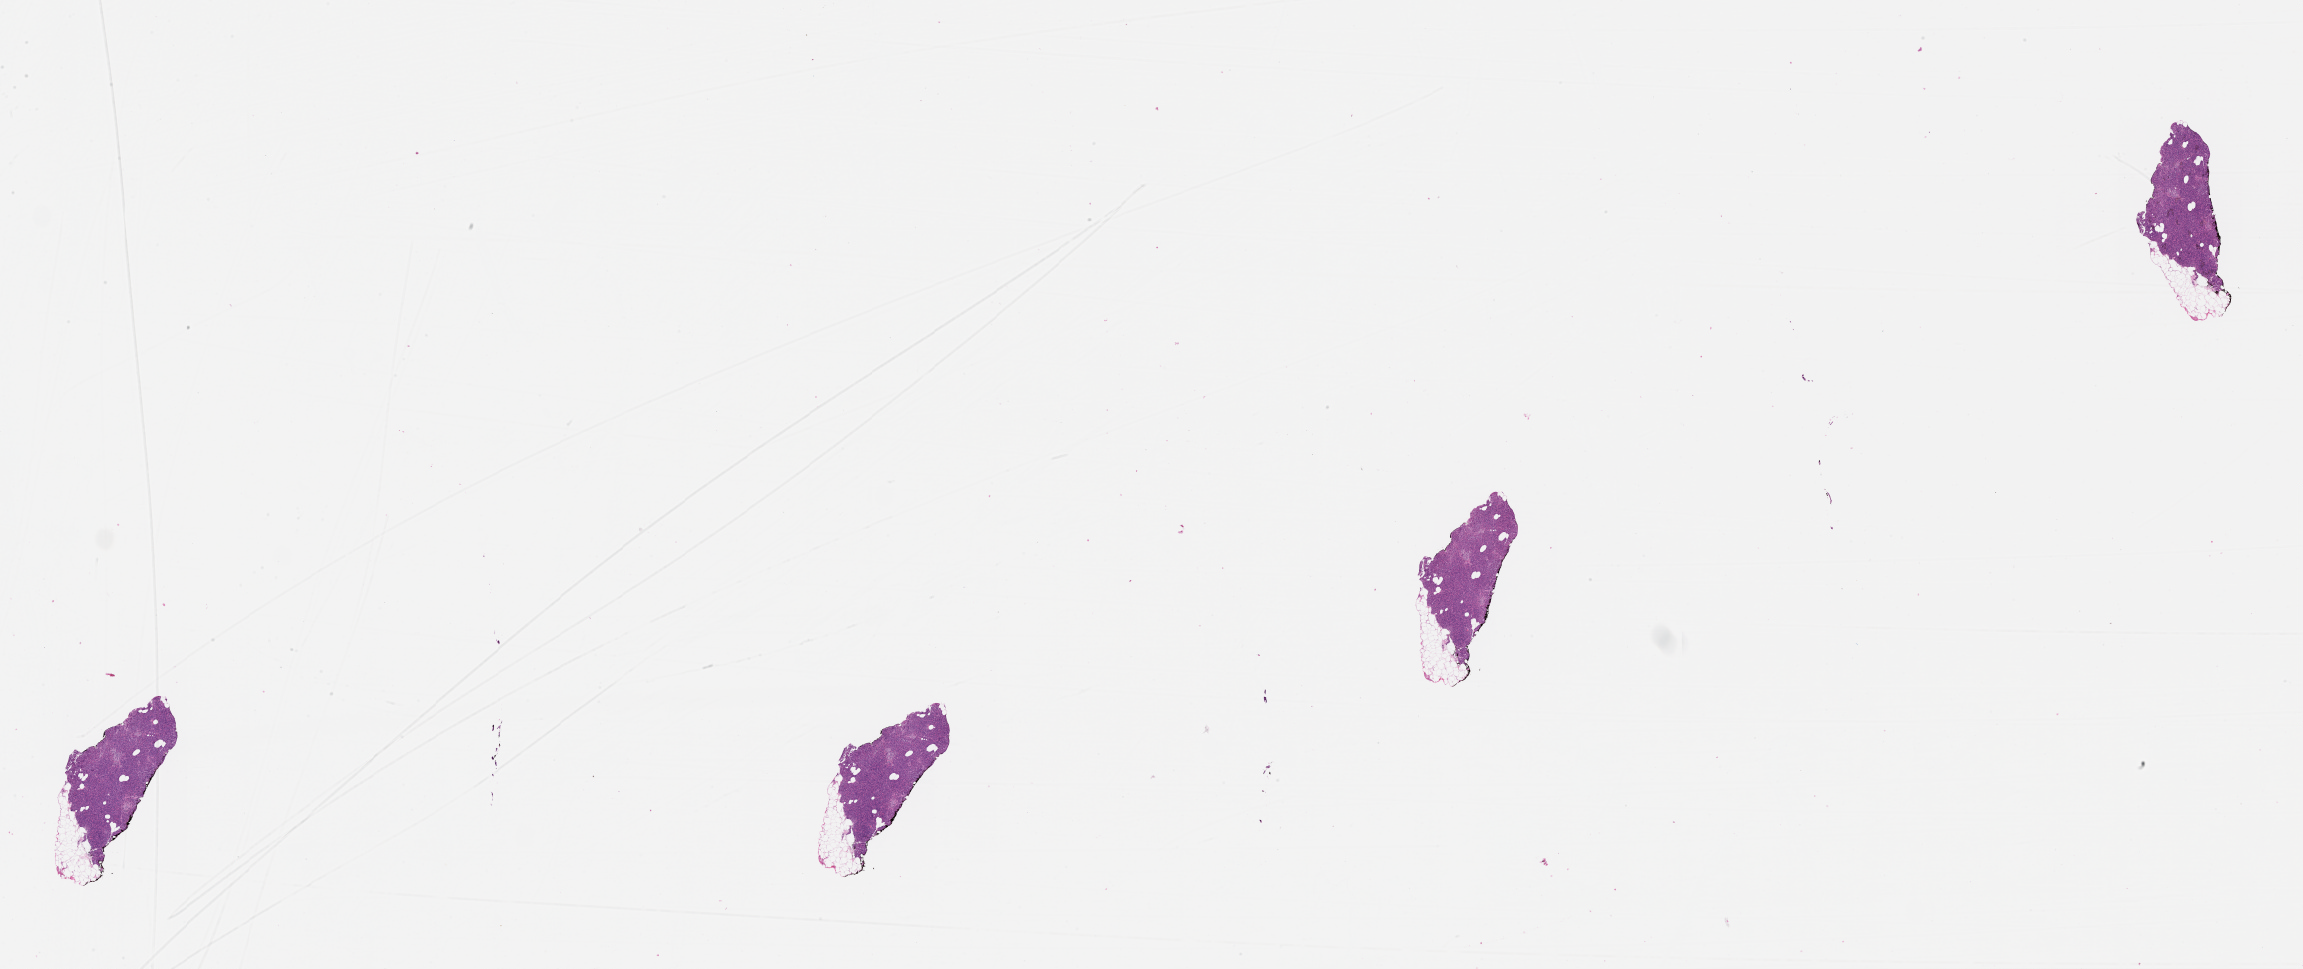
Whole-slide histology image, H&E-stained — a low-resolution overview of the entire scanned area, about 37.1 x 15.6 mm (slide scanned at 20x), pancreas, normal (non-tumour) tissue. 71-year-old female patient.
This section: normal (non-tumour) tissue from the same patient. Patient diagnosis: Infiltrating duct carcinoma, NOS.